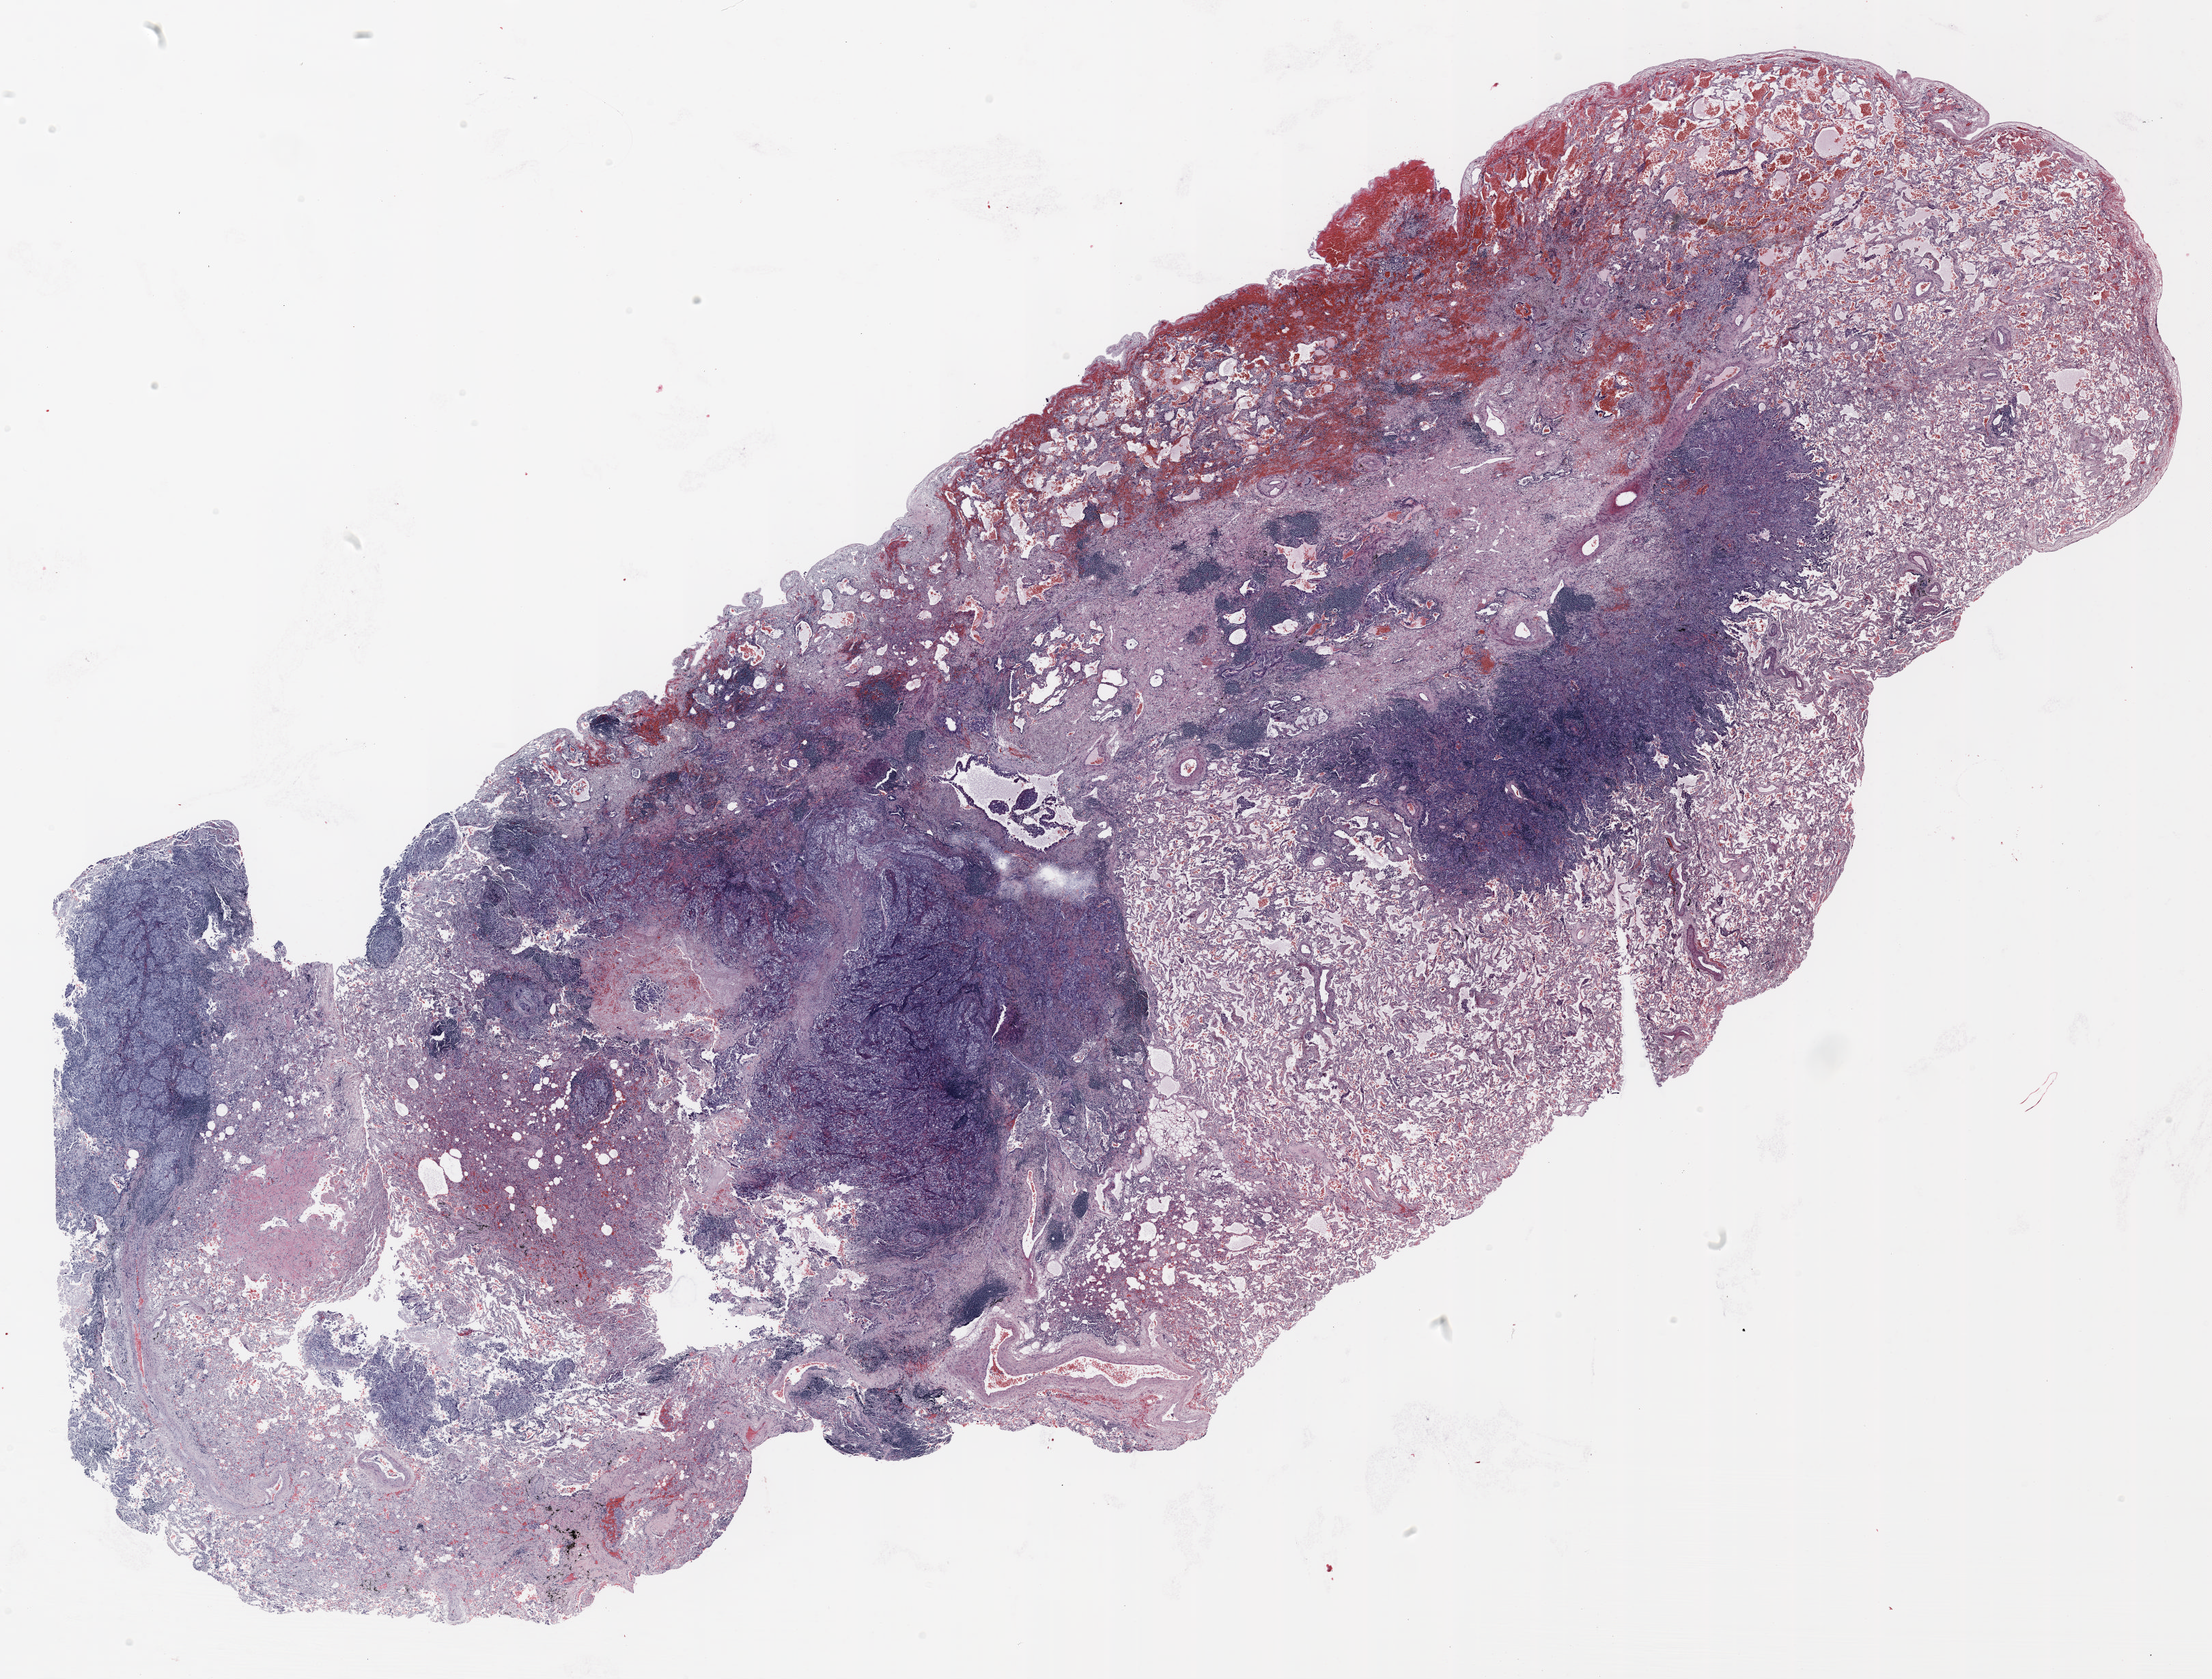
H&E-stained whole-slide image — a low-resolution overview of the entire scanned area, about 26.0 x 19.8 mm. FFPE section. Lung tissue. Female patient, aged 67 at enrolment. Former smoker at enrolment. Grade: poorly differentiated (G3).
- tumour size (pathology): 30 mm
- stage (AJCC 6th edition): IA
- primary tumour location (clinical record): right upper lobe
- participant's lung-cancer diagnosis: Adenocarcinoma with mixed subtypes